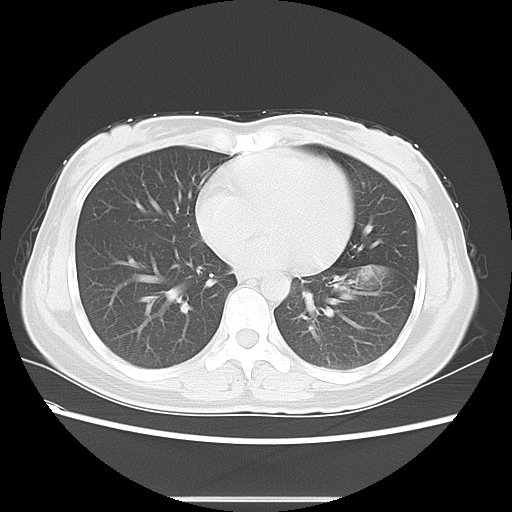
Chest CT, one axial slice. Position 24 of 55 along the scan axis. 120 kVp. Lung window (W 1500 / L -600 HU). 5 mm slice thickness. 512 × 512 image matrix, field of view 350 × 350 mm. Female patient, age 41 years. Case-level facts recorded for this patient, not image findings: clinical TNM (as recorded): T1c N3 M1b.
Annotated regions visible in this slice (bounding box drawn by a radiologist):
- lung tumour (recorded histology: adenocarcinoma): box from (x=347, y=258) to (x=392, y=294) px